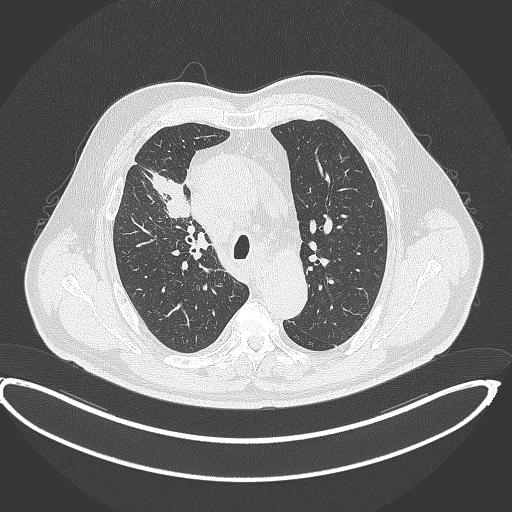
Chest CT, one axial slice. Slice 287 of 390 in the series (ordered by position). Reconstruction kernel B70f. Lung window (W 1500 / L -600 HU). 1 mm slice thickness. 512 × 512 image matrix, field of view 448 × 448 mm. Male patient, age 62 years. From the clinical record (not read from this slice): clinical TNM (as recorded): T1c N3 M1c.
Annotated regions visible in this slice (rectangle marked by the reading radiologist):
- lung tumour (recorded histology: adenocarcinoma): box from (x=148, y=168) to (x=195, y=218) px